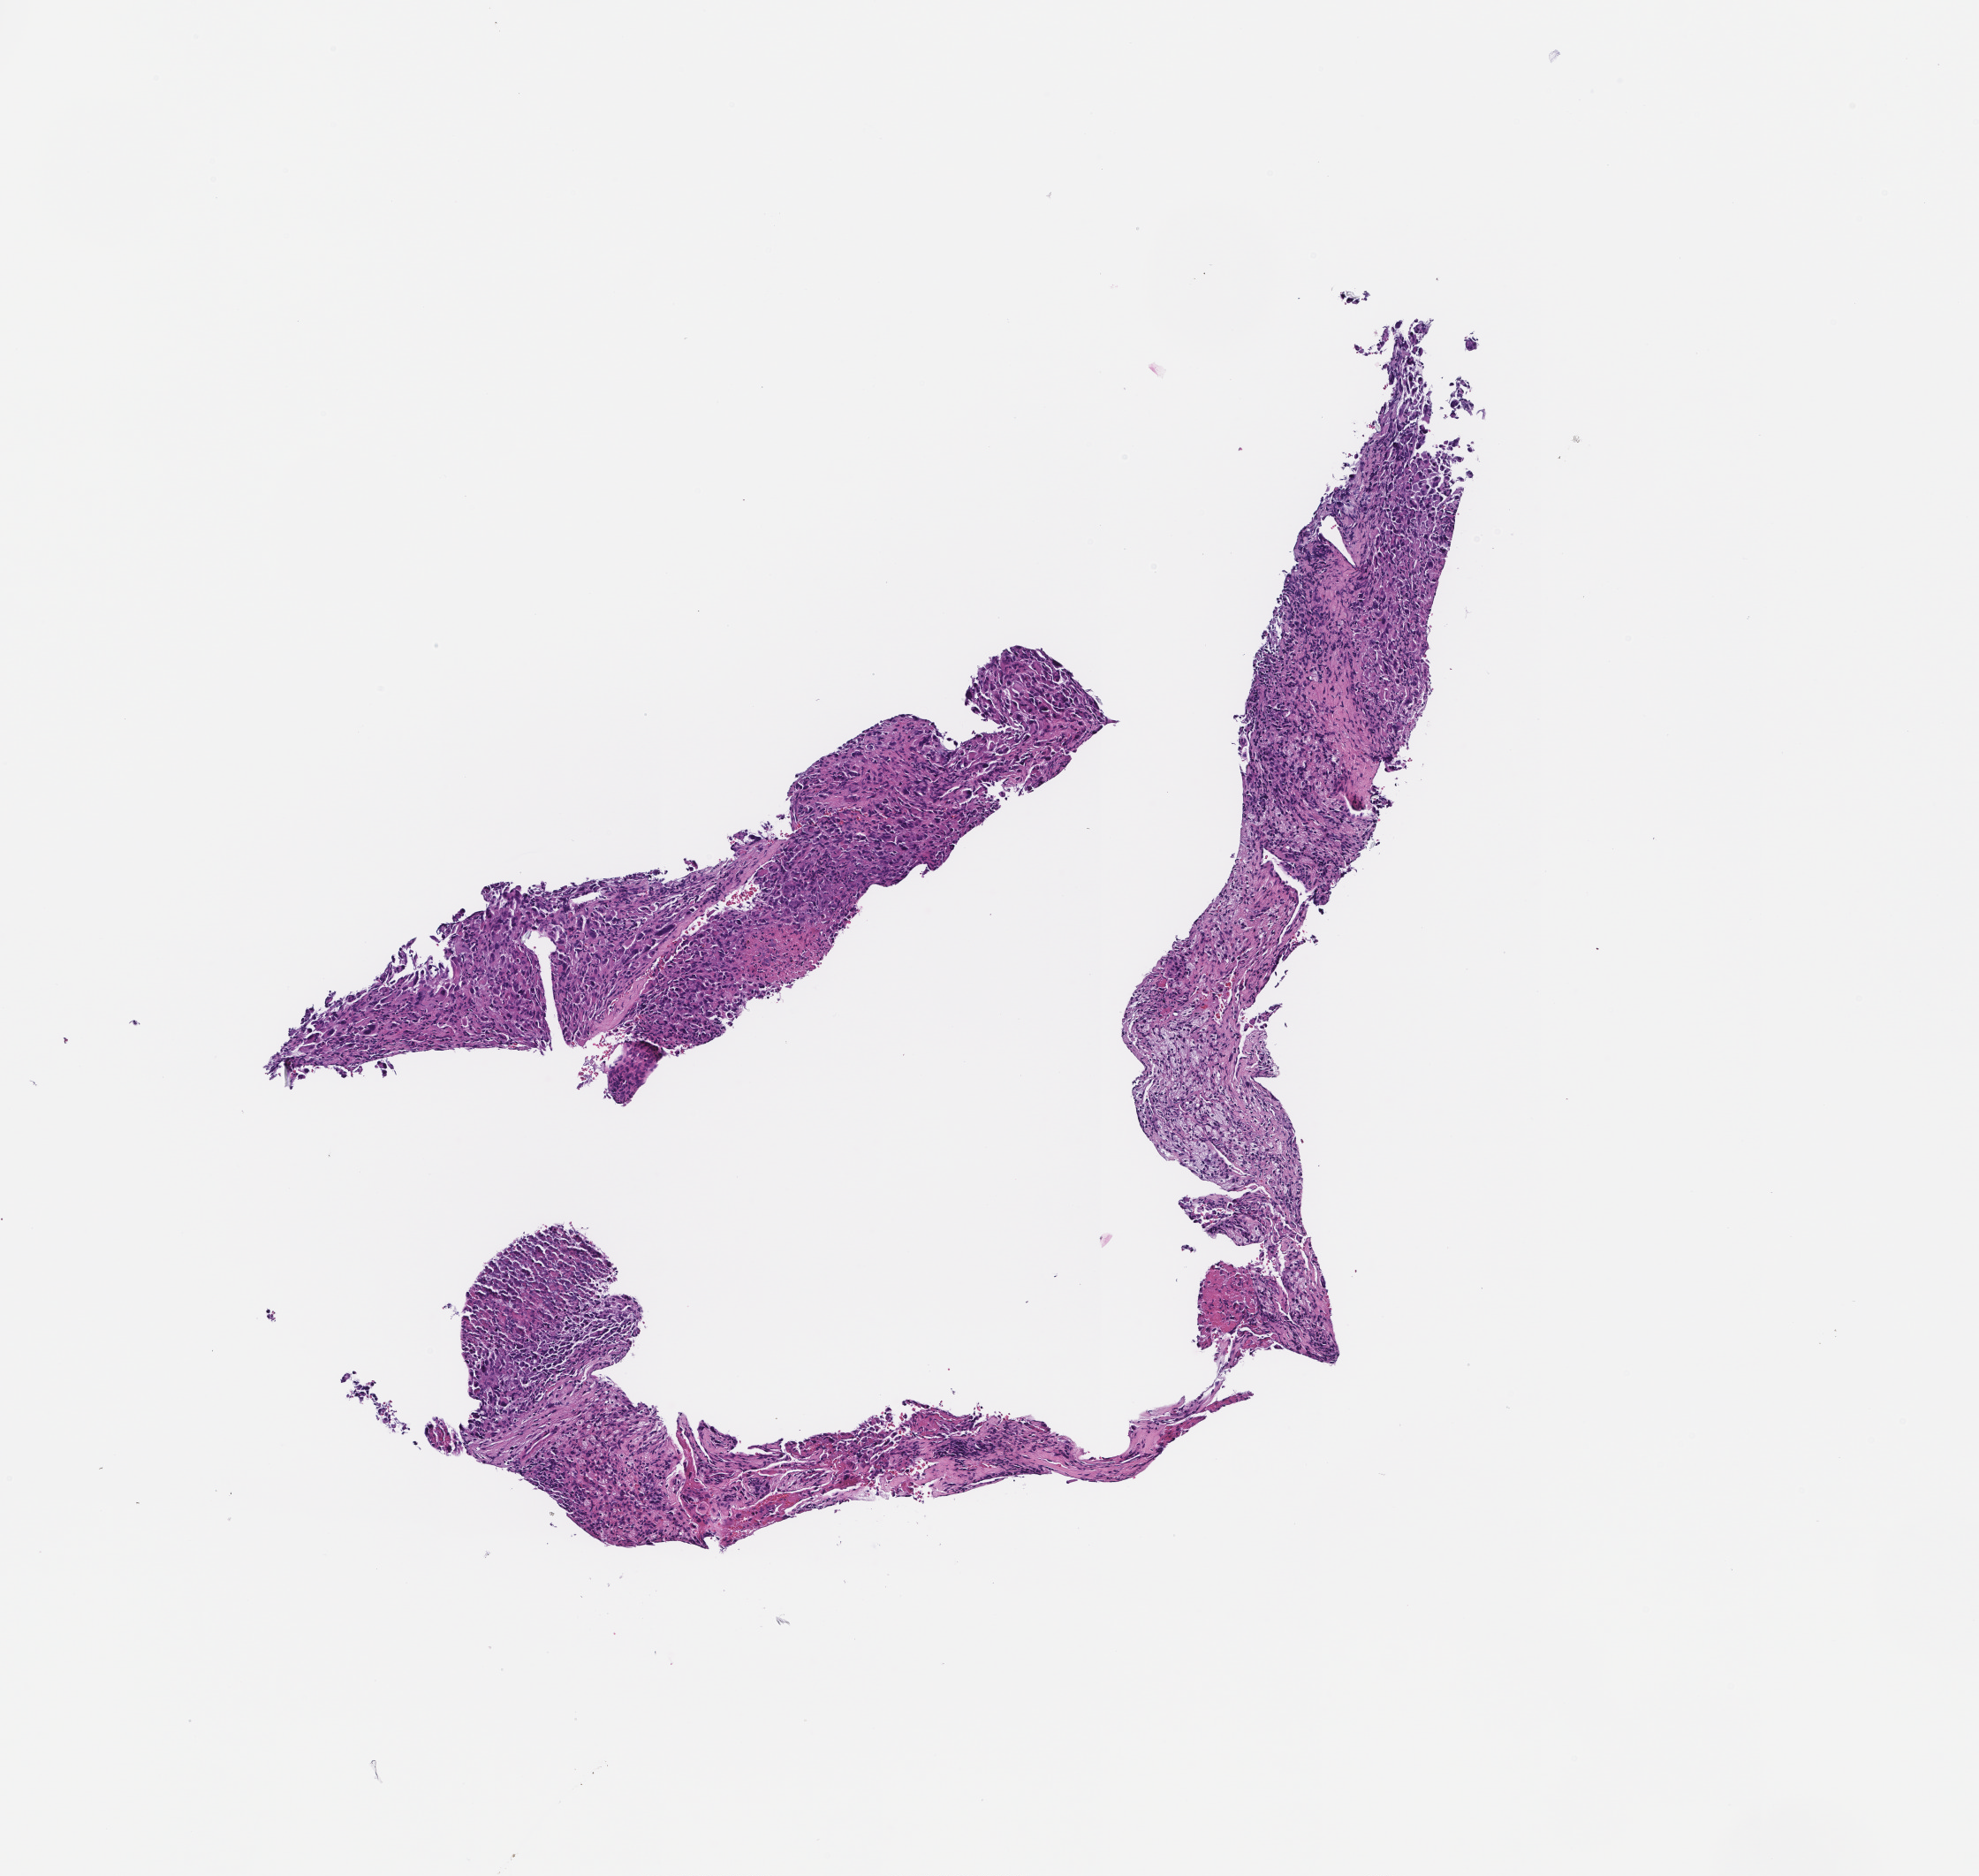
Hematoxylin and eosin (H&E) whole-slide image — low-resolution overview of the scanned area, about 4.5 x 4.3 mm. FFPE section. Collected at disease progression. Patient: male.
This section: metastasis (sampled organ not recorded). Primary diagnosis of the patient: Non-Small Cell Lung Carcinoma.